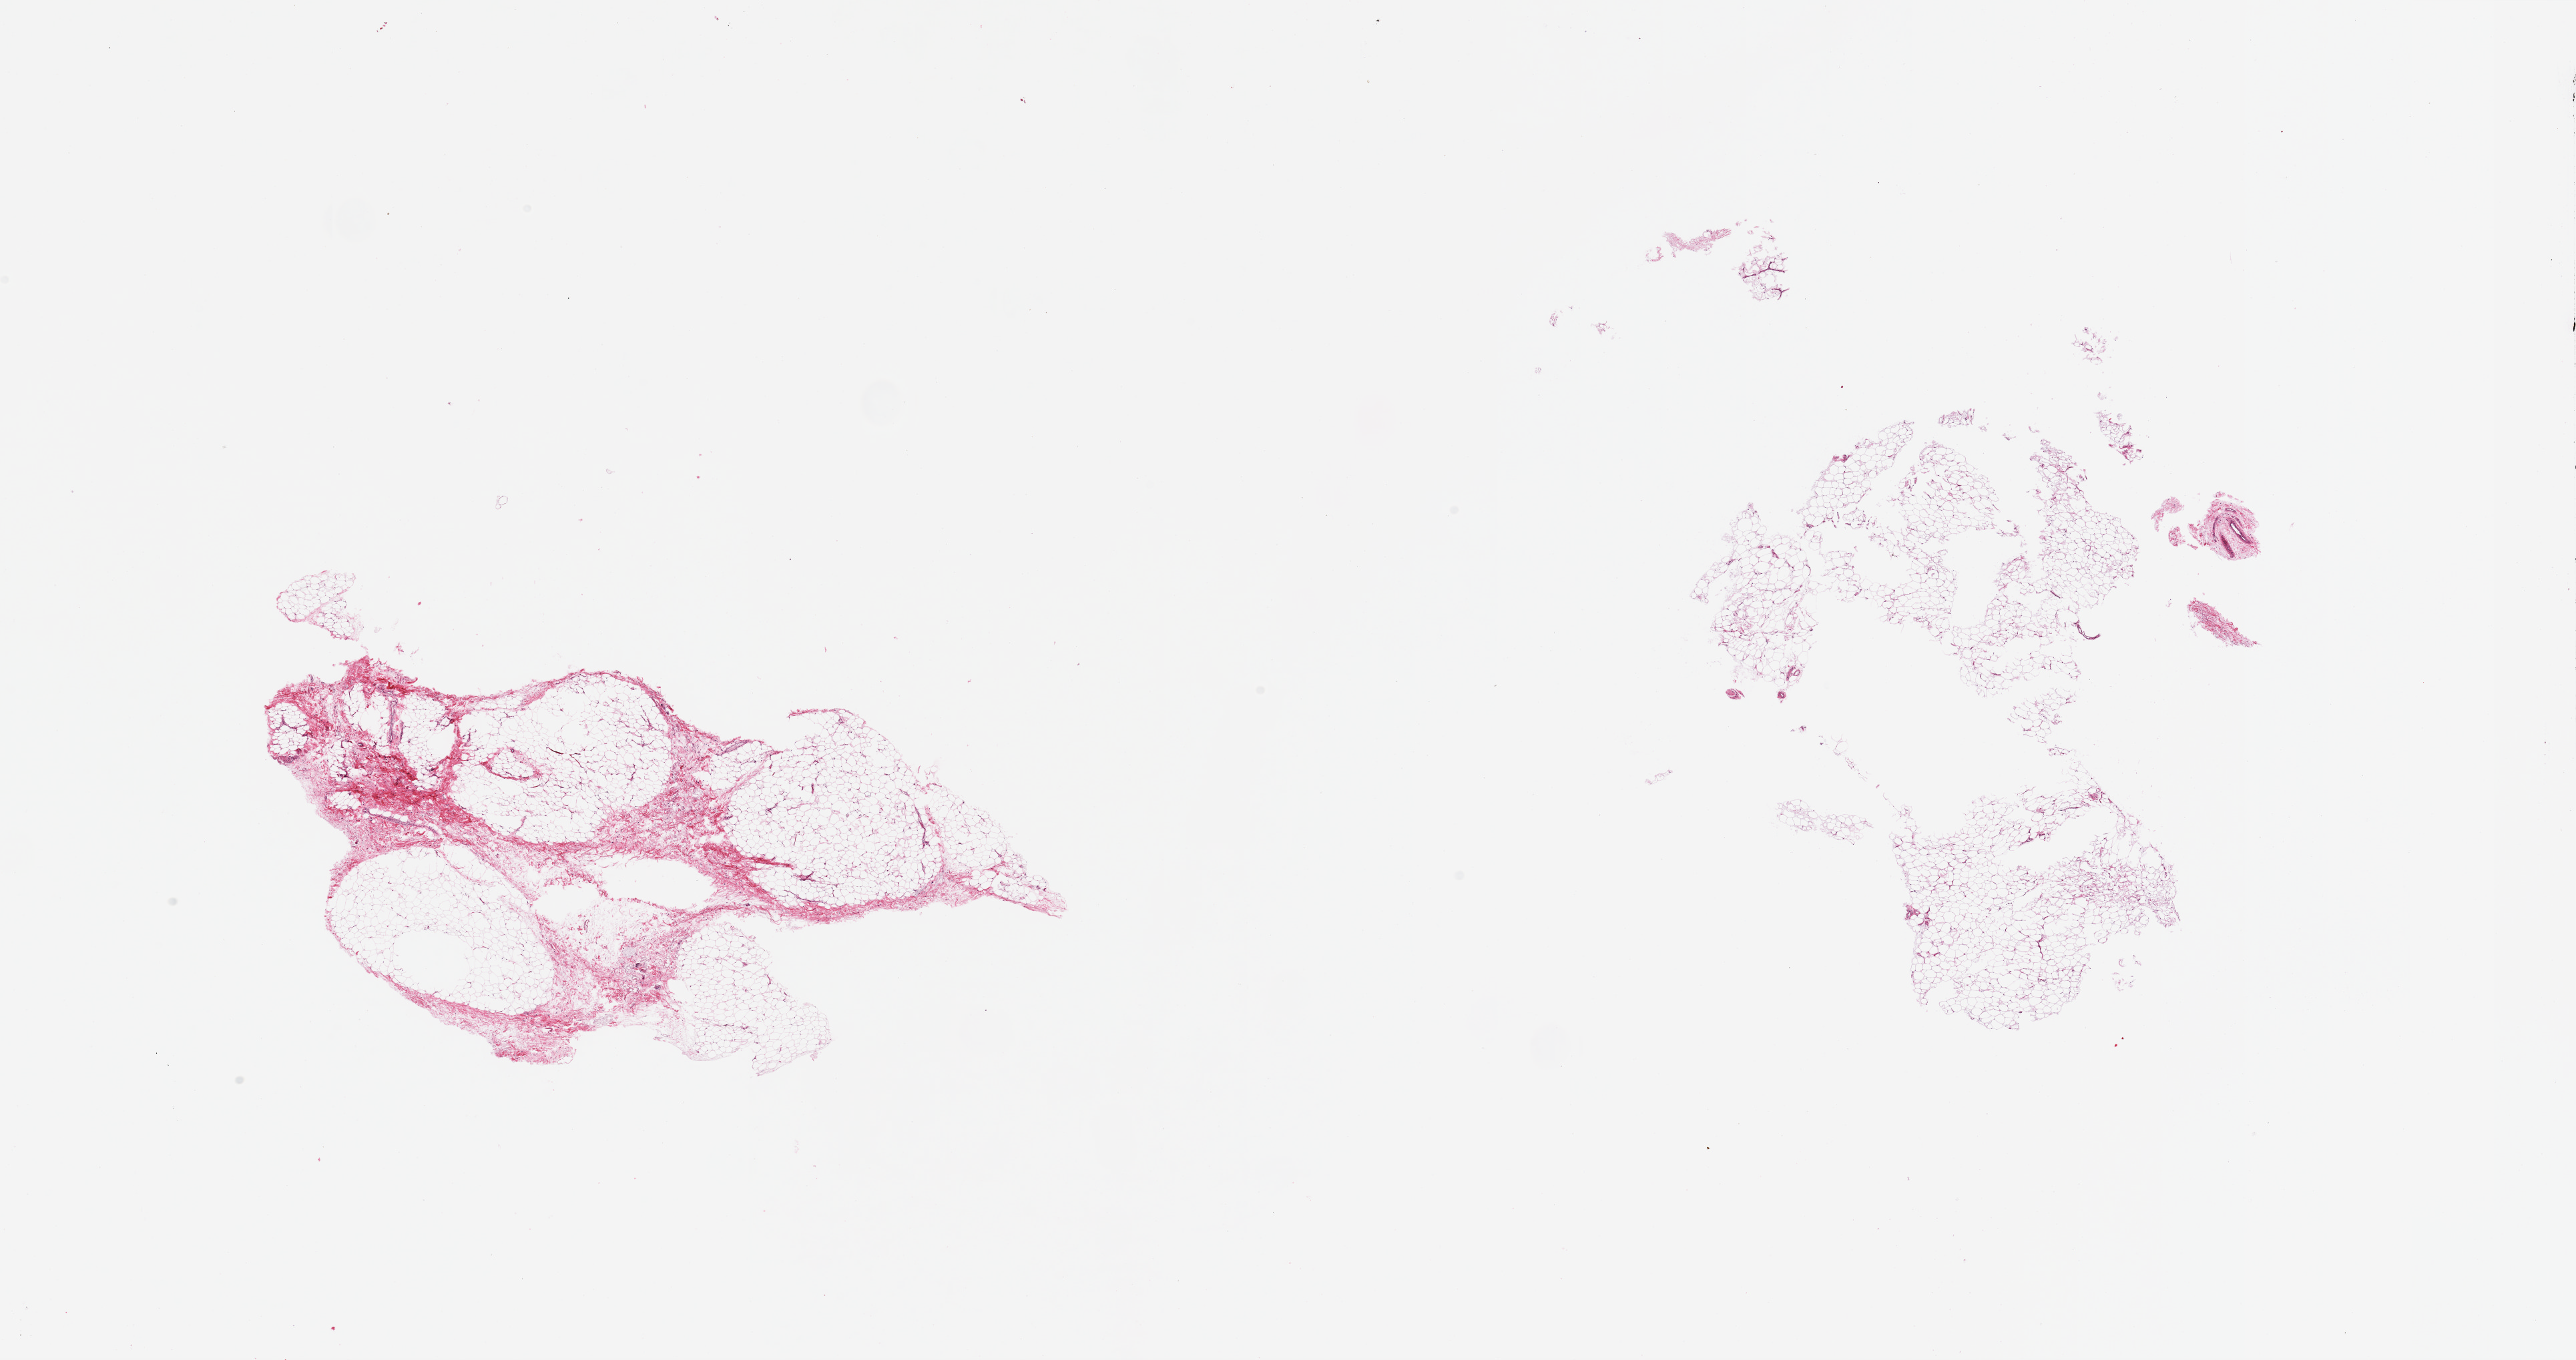
Whole-slide image, hematoxylin and eosin (H&E) stain, shown as a low-resolution overview of the whole scanned area (about 30.5 x 16.1 mm); PAXgene-fixed paraffin-embedded (PFPE) section; target tissue: adipose tissue; donor tissue sample. Donor: male.
- reviewer comment on this tissue sample: 2 pieces; 10% fibrous content in one